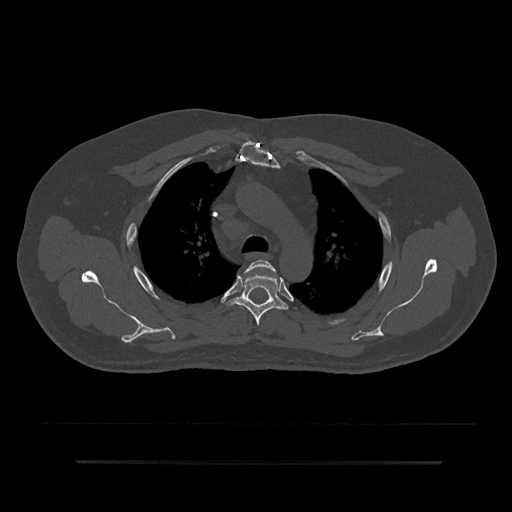
CT including the spine, one axial slice; position 622 of 797 along the scan axis; reconstruction kernel Br40s/3; 120 kVp; bone window (W 1800 / L 400 HU); 0.5 mm slice thickness; 512 × 512 image matrix. Male patient, age 59 years. From the clinical record (not read from this slice): primary cancer: bile ducts; vertebrae with lytic lesions (as recorded): T10.
Structures marked on this image (semi-automatically segmented with operator editing):
- T3 vertebra: bounding box <246,260,277,277> (left, top, right, bottom; pixels)
- T4 vertebra: <226,270,289,326>